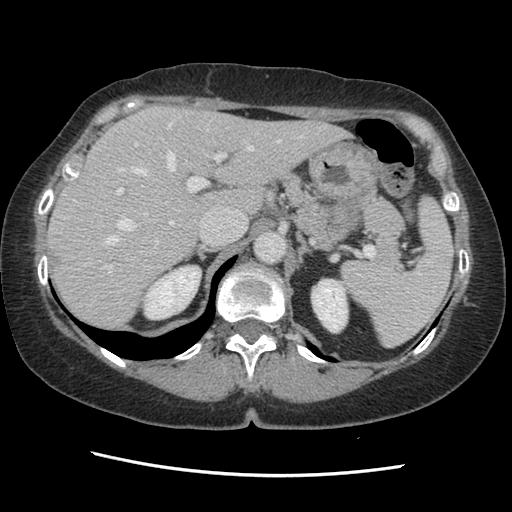
Contrast-enhanced abdominal CT, one axial slice; position 94 of 141 along the scan axis; 120 kVp; soft-tissue window (W 400 / L 40 HU); 2.5 mm slice thickness; 512 × 512 image matrix, field of view 330 × 330 mm. Female patient, age 61 years. Case-level facts recorded for this patient, not image findings: diagnosis: colorectal cancer liver metastases, imaged before liver resection; multiple liver metastases: no; largest metastasis: 2.4 cm; disease in both lobes: no.
Annotated regions visible in this slice (outlined manually by an expert reader):
- hepatic veins: bounding box (x1, y1, x2, y2) in pixels: (106, 121, 303, 245)
- liver: (49, 107, 345, 331)
- planned liver remnant (the part of the liver to remain after resection): (49, 107, 345, 331)
- portal vein (with intrahepatic branches): (103, 142, 227, 274)